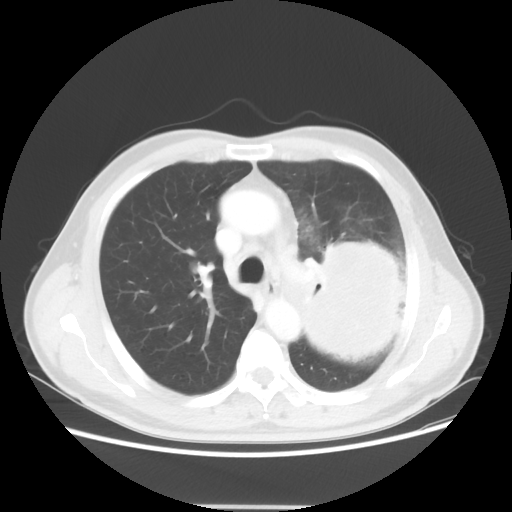
Chest CT, one axial slice. Slice 36 of 53 in the series (ordered by position). Reconstruction kernel STANDARD. Lung window (W 1500 / L -600 HU). 5 mm slice thickness. 512 × 512 image matrix, field of view 391 × 391 mm. Patient: male, 60 years. Case-level facts recorded for this patient, not image findings: clinical TNM (as recorded): T4 N1 M1a.
Annotated regions visible in this slice (rectangle marked by the reading radiologist):
- lung tumour (recorded histology: large cell carcinoma): bounding box <289,227,412,365> (left, top, right, bottom; pixels)